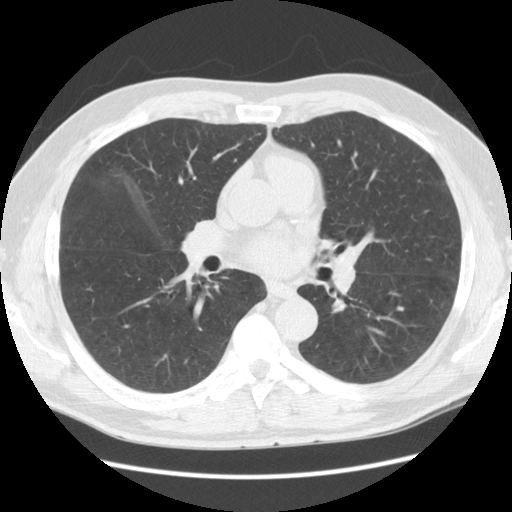
Low-dose screening chest CT, axial slice. Second annual screen. Lung window (W 1500 / L -600 HU). 2.5 mm slice thickness. Male, age 60 years at enrolment. Current smoker at enrolment.
Expert reader's lesion annotation, bounding box (x1, y1, x2, y2) in pixels: (387, 297, 416, 324). The screening reader recorded 4 non-calcified nodules or masses ≥4 mm on this exam (right lower lobe, right middle lobe, left lower lobe, left upper lobe); which of them this box marks is not recorded. Participant outcome: lung cancer diagnosed 594 days after this screen (after the third annual screen) — large cell neuroendocrine carcinoma, left lower lobe, poorly differentiated (G3), stage IB (AJCC 6th edition), 33 mm at pathology.